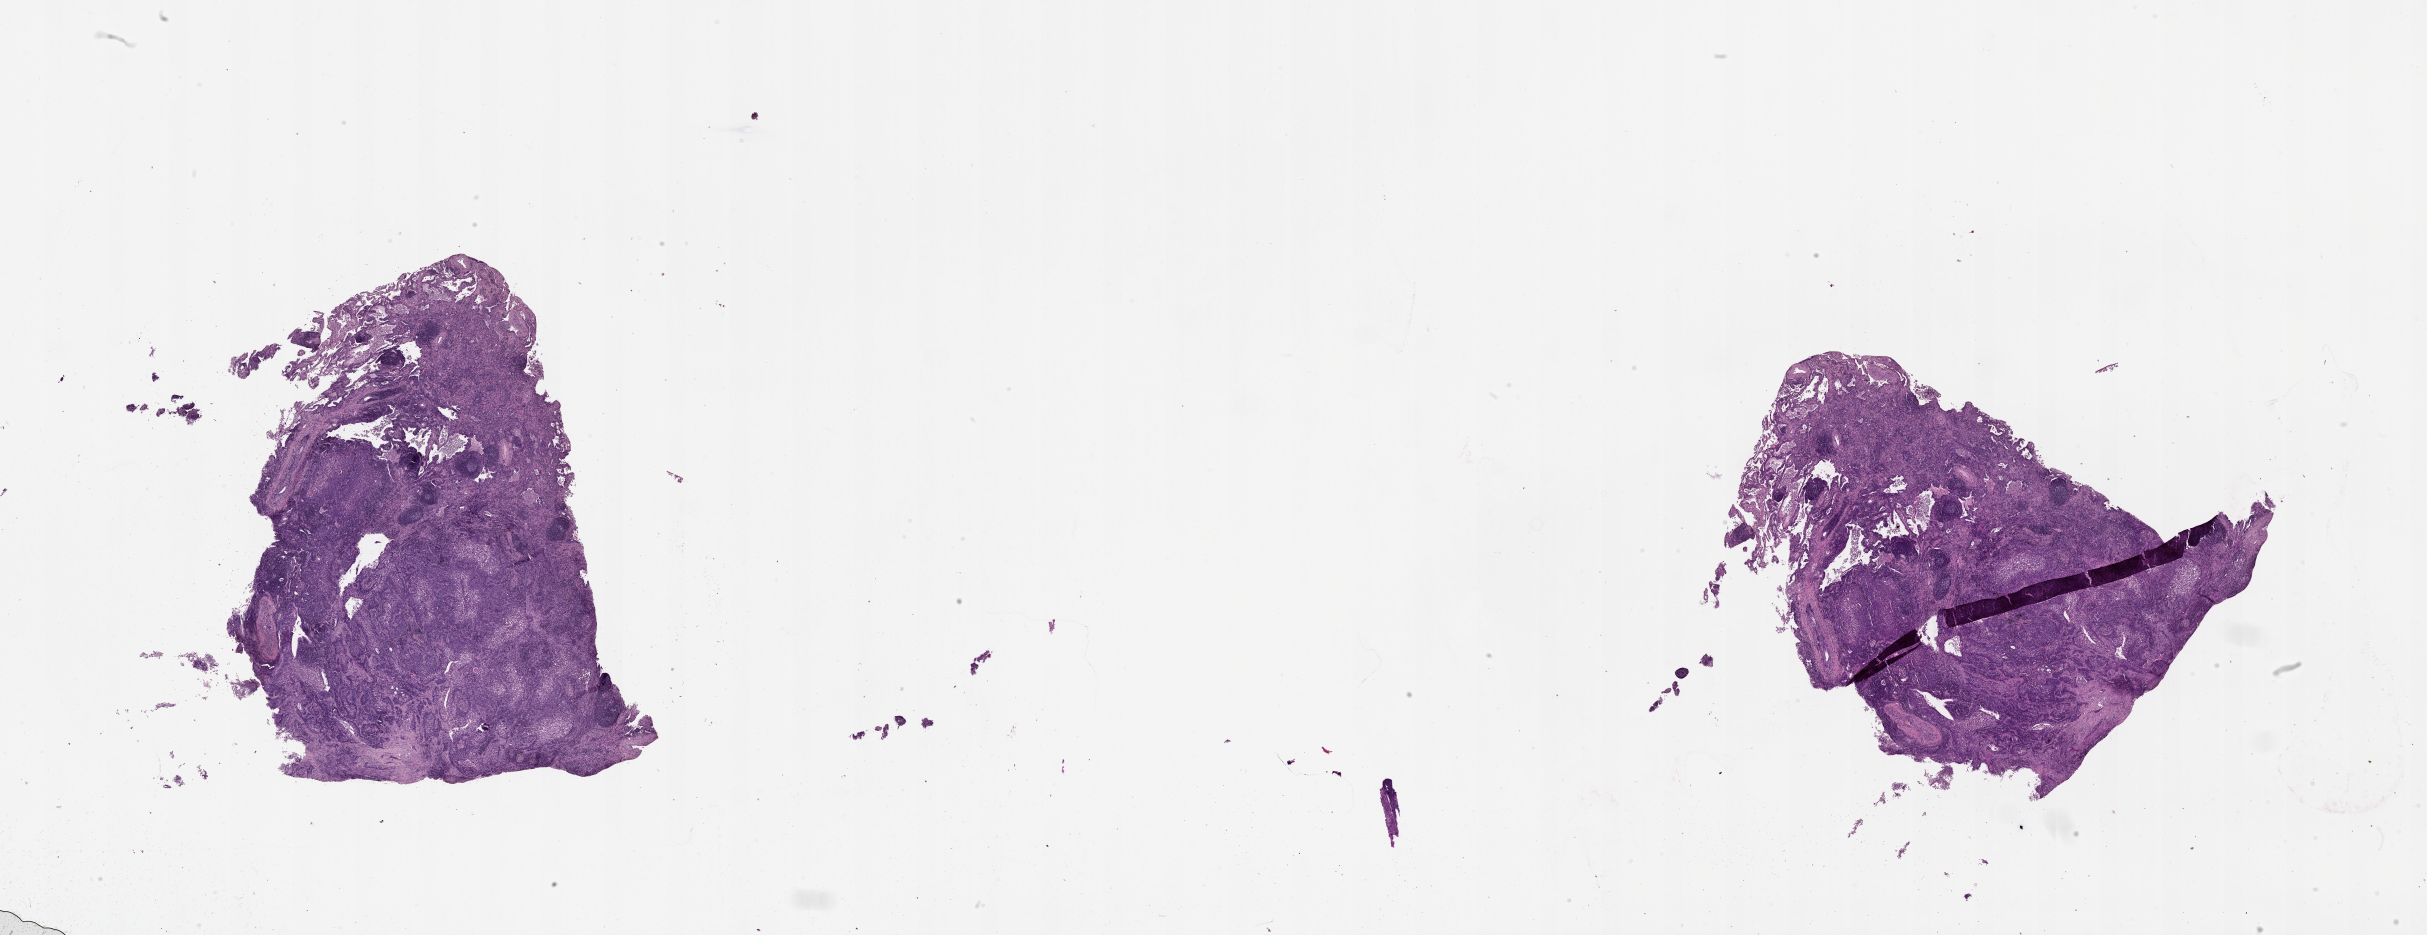
H&E whole-slide image, shown as a low-resolution overview of the whole scanned area (about 39.1 x 15.1 mm, from a 20x scan). Tumour tissue sample, lung. 66-year-old male patient.
Patient diagnosis (cohort enrolment): squamous cell carcinoma (lung).